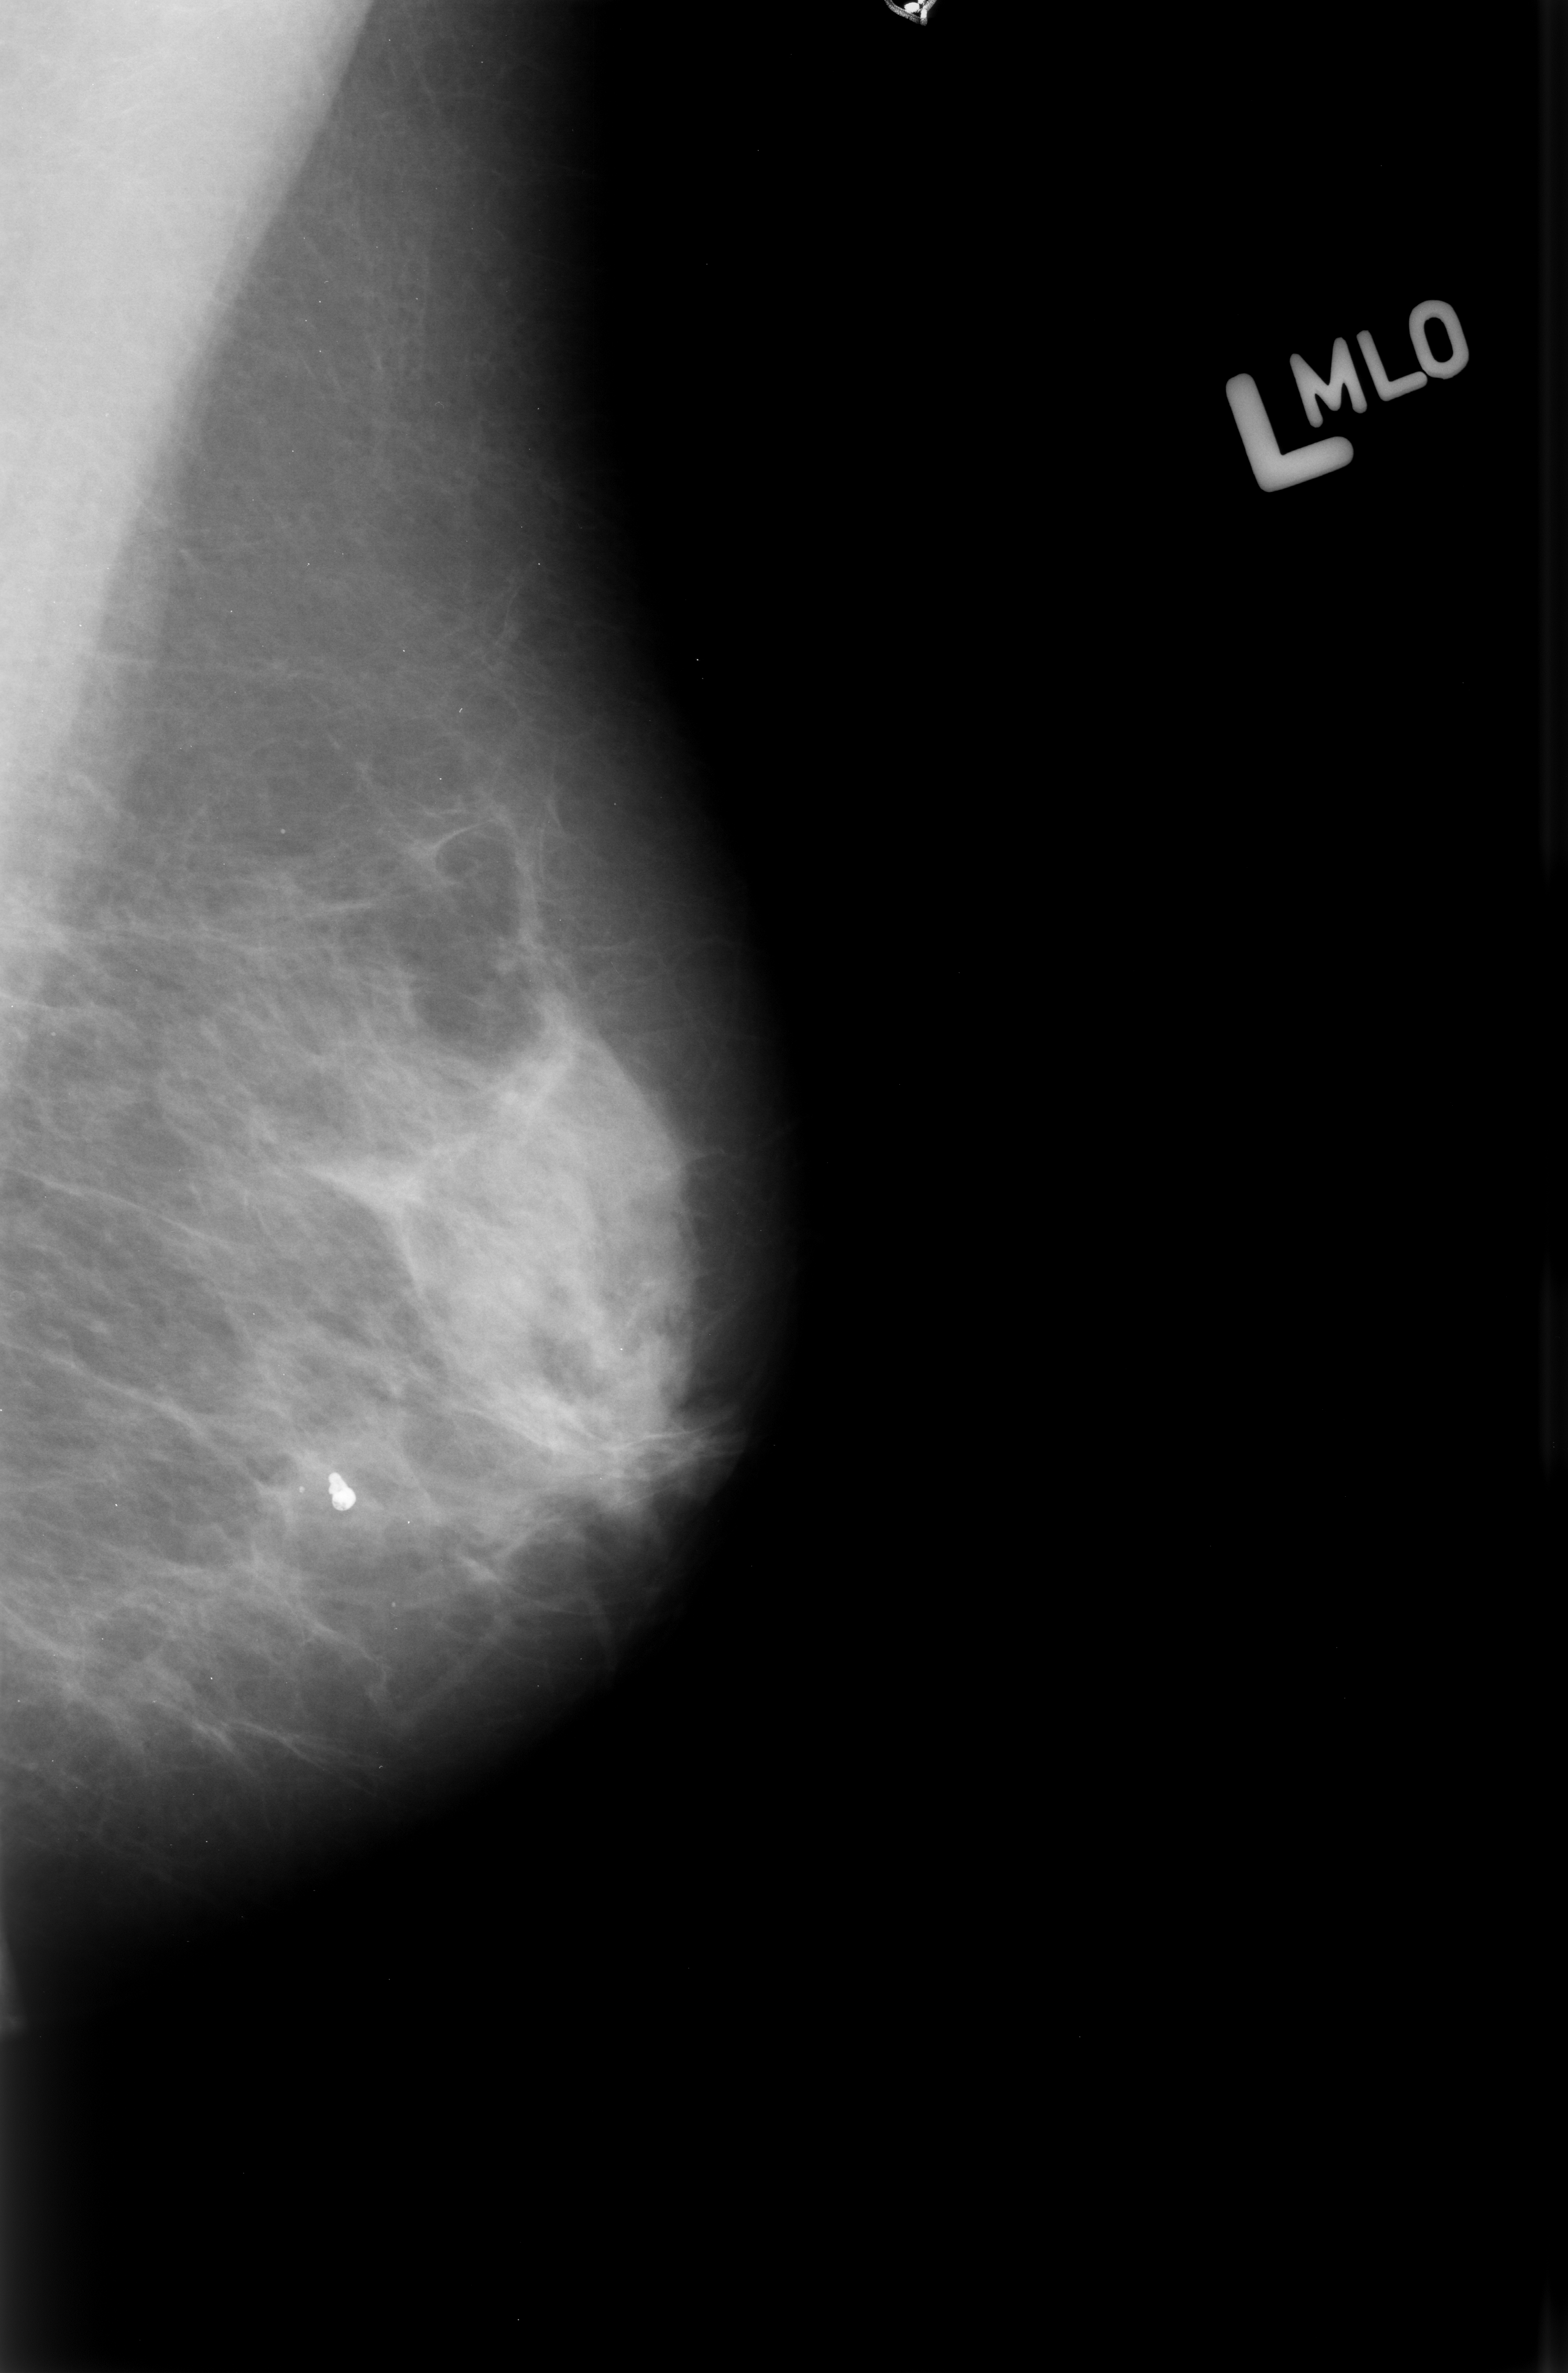
Mammogram (digitized film); left breast; MLO view.
- Marked abnormality: calcifications, morphology coarse; BI-RADS assessment category 2; subtlety rating 5 on a 1 (subtle) to 5 (obvious) scale; benign without callback (not worked up further).